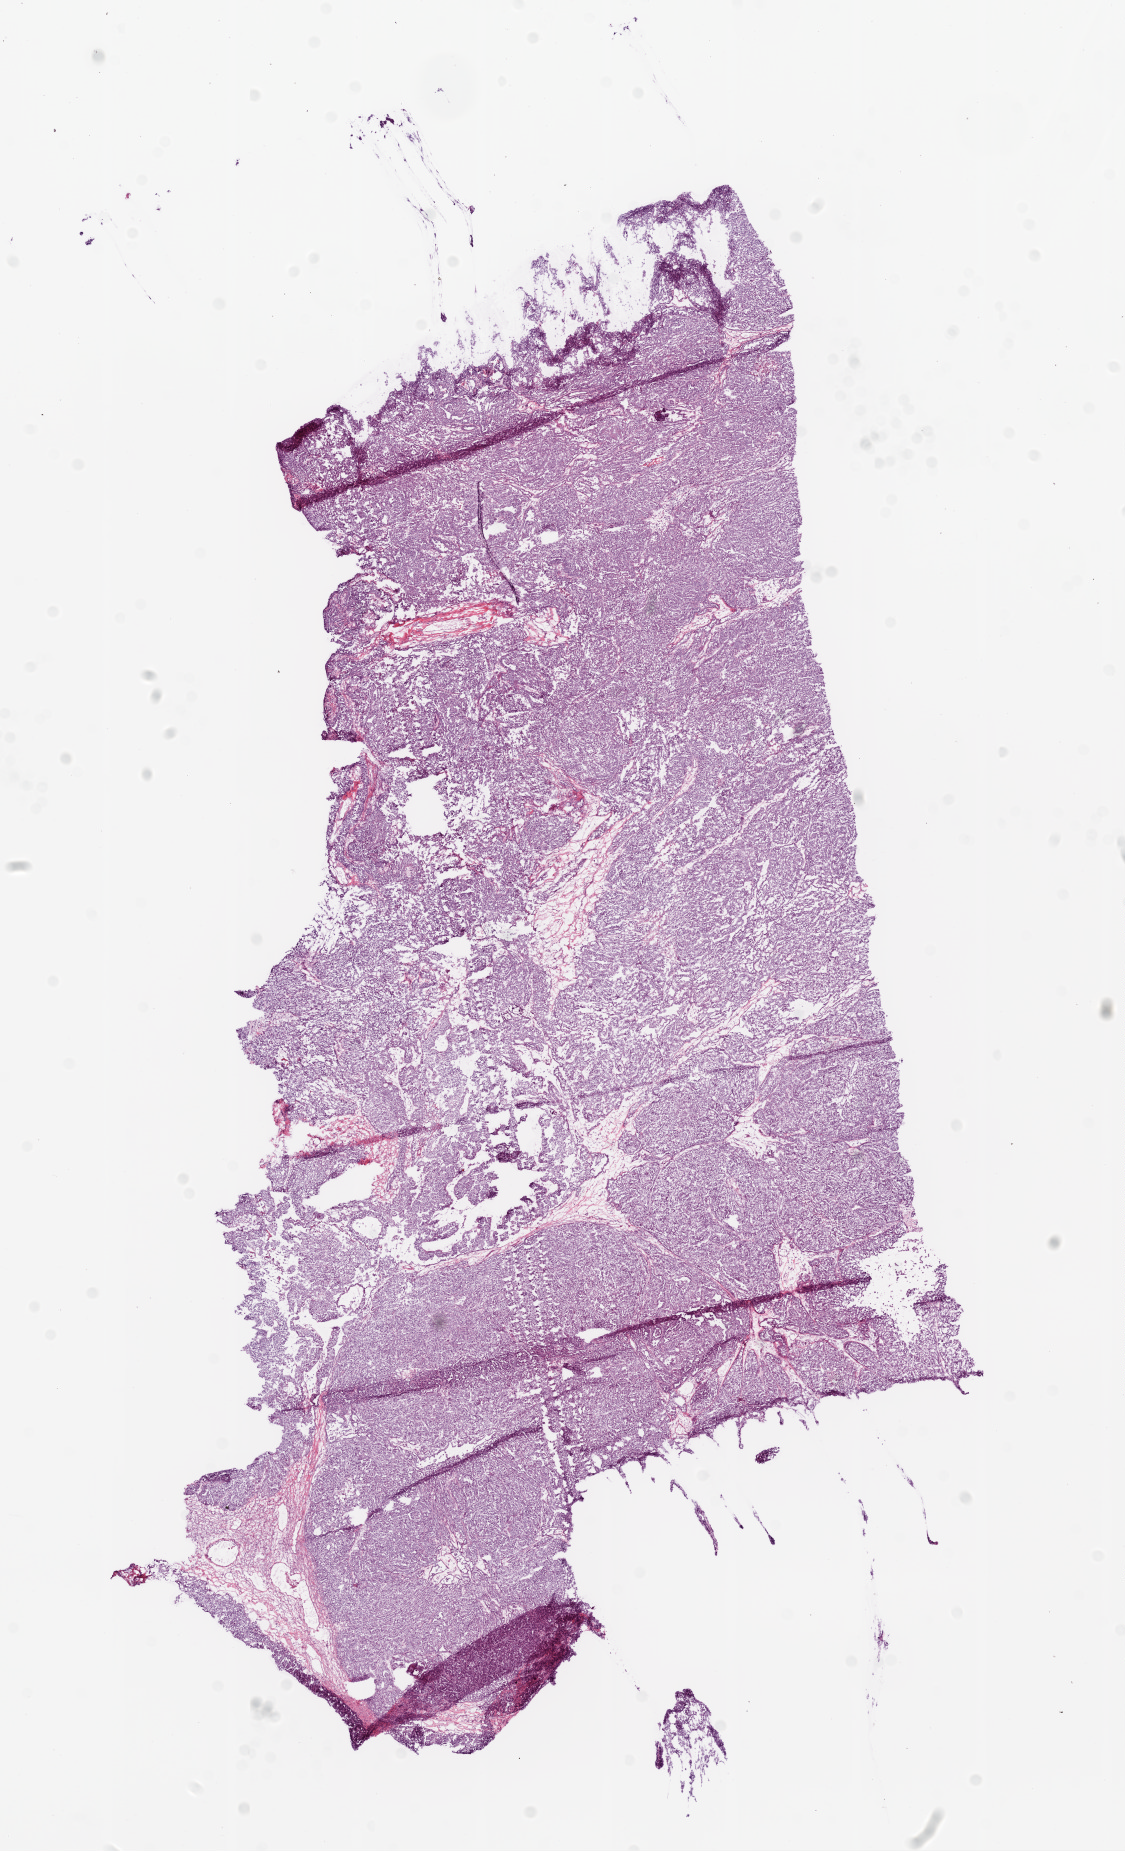
Whole-slide histology image, H&E-stained — whole scanned area (about 9.0 x 14.9 mm) shown as a low-resolution overview, frozen section, ovary, primary tumour sample. Female, age 59 years at initial diagnosis. Histologic grade: G3 (poorly differentiated). Slide review estimates, as recorded: tumour cells 95%, tumour nuclei 95%, normal cells 0%, stromal cells 5%, necrosis 0%.
Diagnosis: Serous cystadenocarcinoma, NOS. FIGO stage: IV. Laterality: bilateral.